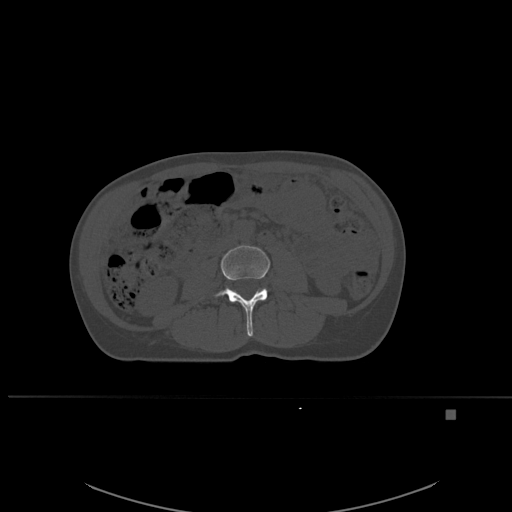
CT including the spine, one axial slice. Slice 211 of 537 in the series (ordered by position). Bone window (W 1800 / L 400 HU). 1.5 mm slice thickness. 512 × 512 image matrix. Female patient, age 45 years. Case-level facts recorded for this patient, not image findings: primary cancer: lung.
Structures marked on this image (semi-automatic segmentation, software-assisted and operator-edited):
- L3 vertebra: bounding box (x1, y1, x2, y2) in pixels: (214, 245, 270, 337)